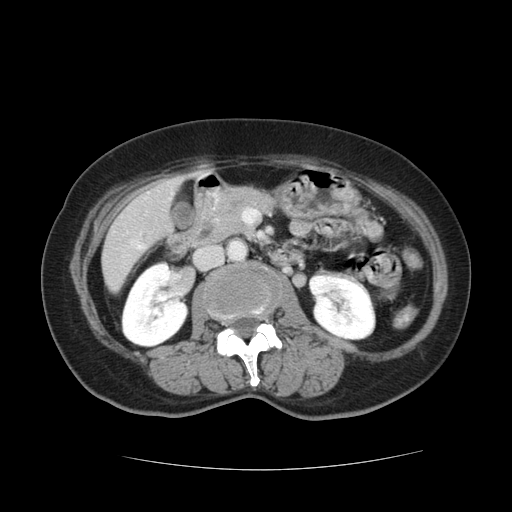
Contrast-enhanced abdominal CT, one axial slice; position 40 of 128 along the scan axis; 120 kVp; intravenous contrast given; soft-tissue window (W 400 / L 40 HU); 2.5 mm slice thickness; 512 × 512 image matrix, field of view 366 × 366 mm. Female patient, age 67 years. Case-level facts recorded for this patient, not image findings: diagnosis: colorectal cancer liver metastases, imaged before liver resection; multiple liver metastases: yes; largest metastasis: 3 cm.
Annotated regions visible in this slice (outlined manually by an expert reader):
- liver: bounding box [x1, y1, x2, y2] px = [102, 176, 181, 290]
- planned liver remnant (the part of the liver to remain after resection): [102, 220, 152, 290]